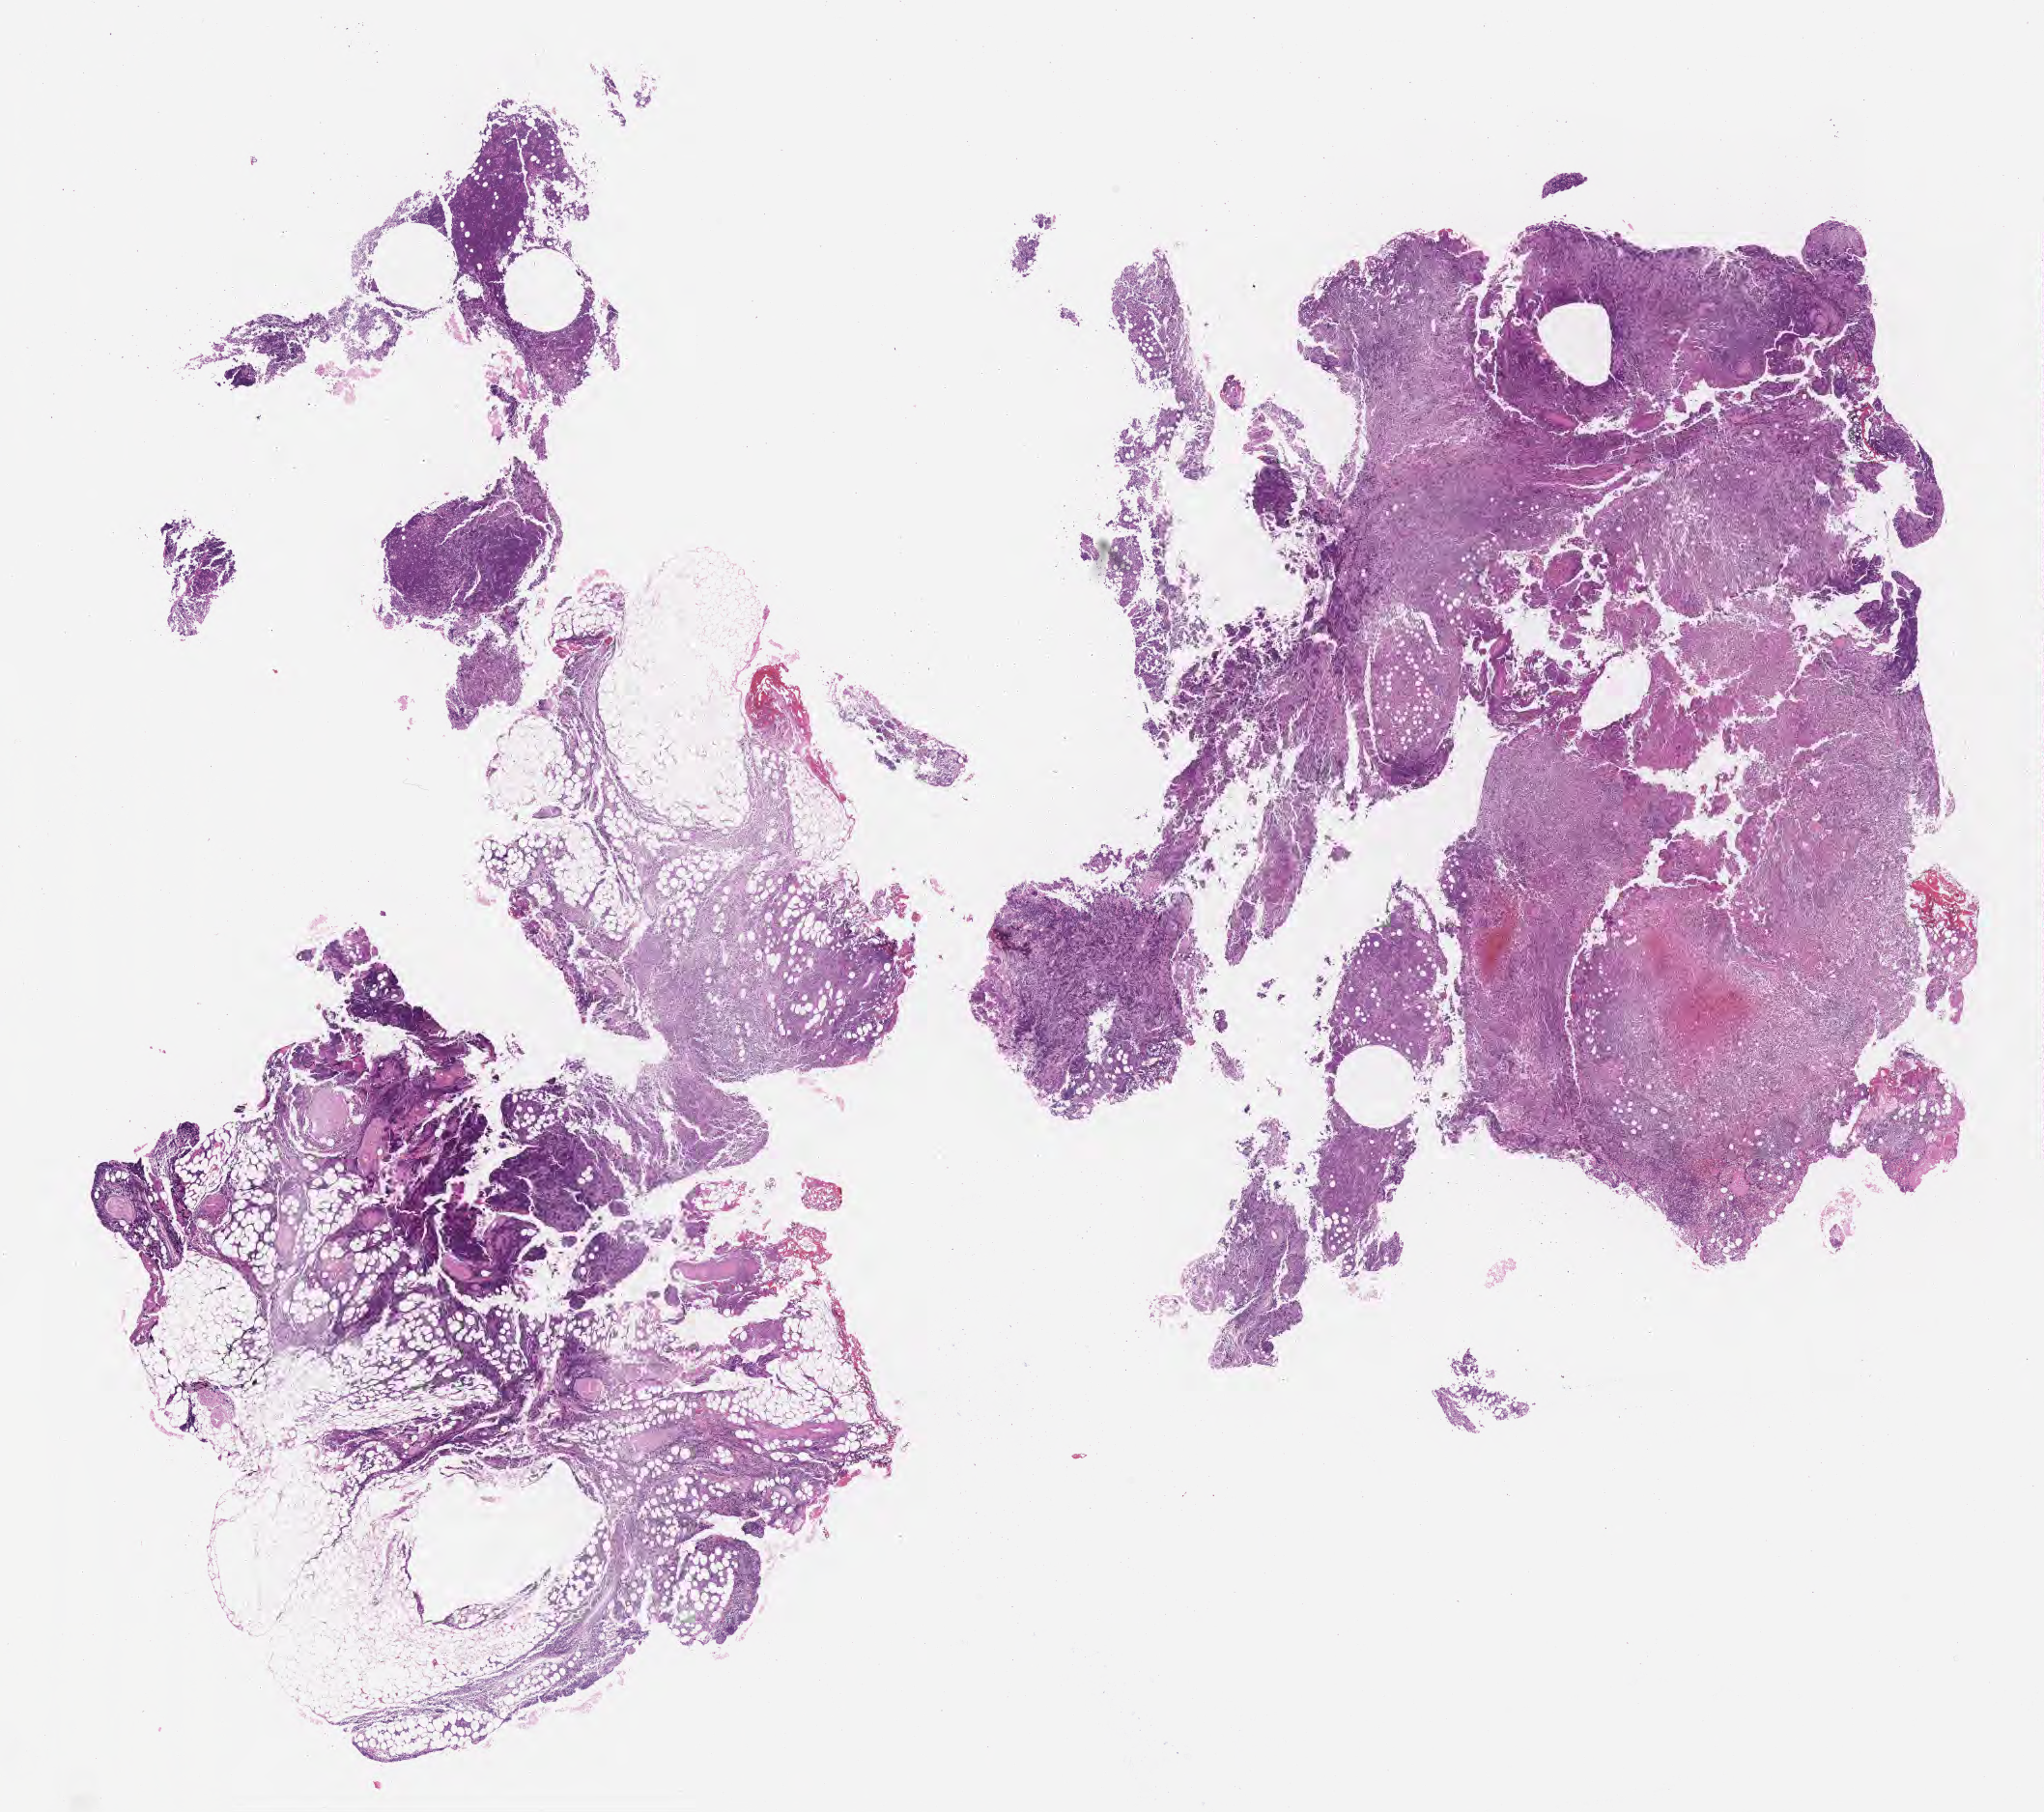
H&E whole-slide image — whole scanned area (about 17.1 x 15.2 mm) shown as a low-resolution overview. FFPE section. Specimen: primary tumor. Female patient, aged 70. Composition of this section per pathologist review: tumor cells 80%, tumor nuclei 90%, stromal cells 5%, necrosis 5%, normal cells 10%. Inflammatory infiltration, as recorded: lymphocyte infiltration 50%, monocyte infiltration 20%, neutrophil infiltration 10%.
Diagnosis: Burkitt lymphoma, NOS. Section: bottom of the tissue portion. Ann Arbor stage (patient): Stage II.